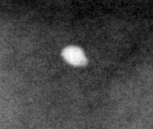
Crop from a digitized film mammogram around one marked abnormality; left breast; CC view.
- Calcifications, morphology round and regular / lucent center / punctate, distribution diffusely scattered; BI-RADS assessment category 2; benign without callback (not worked up further).